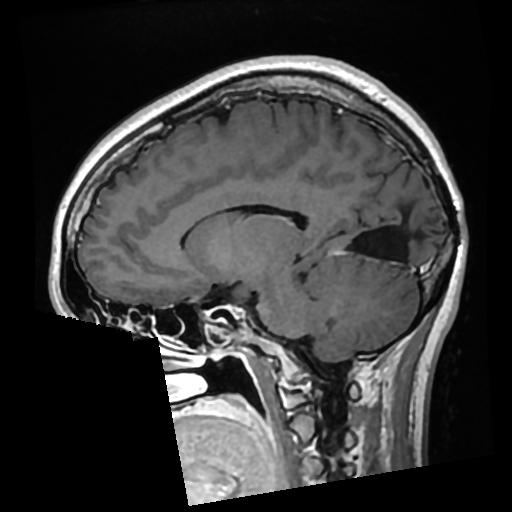
Brain MRI from a brain-tumour surgery series, one sagittal slice; slice 123 of 276 in the series (ordered by position); T1-weighted post-contrast; 512 × 512 image matrix, field of view 250 × 250 mm. From the clinical record (not read from this slice): histopathology: Glioma with ependymal features; WHO grade: 2; tumour location: Left Parietal.
Outlined on this slice (manually delineated by an expert):
- previous resection cavity: bounding box (x1, y1, x2, y2) in pixels: (355, 231, 404, 258)